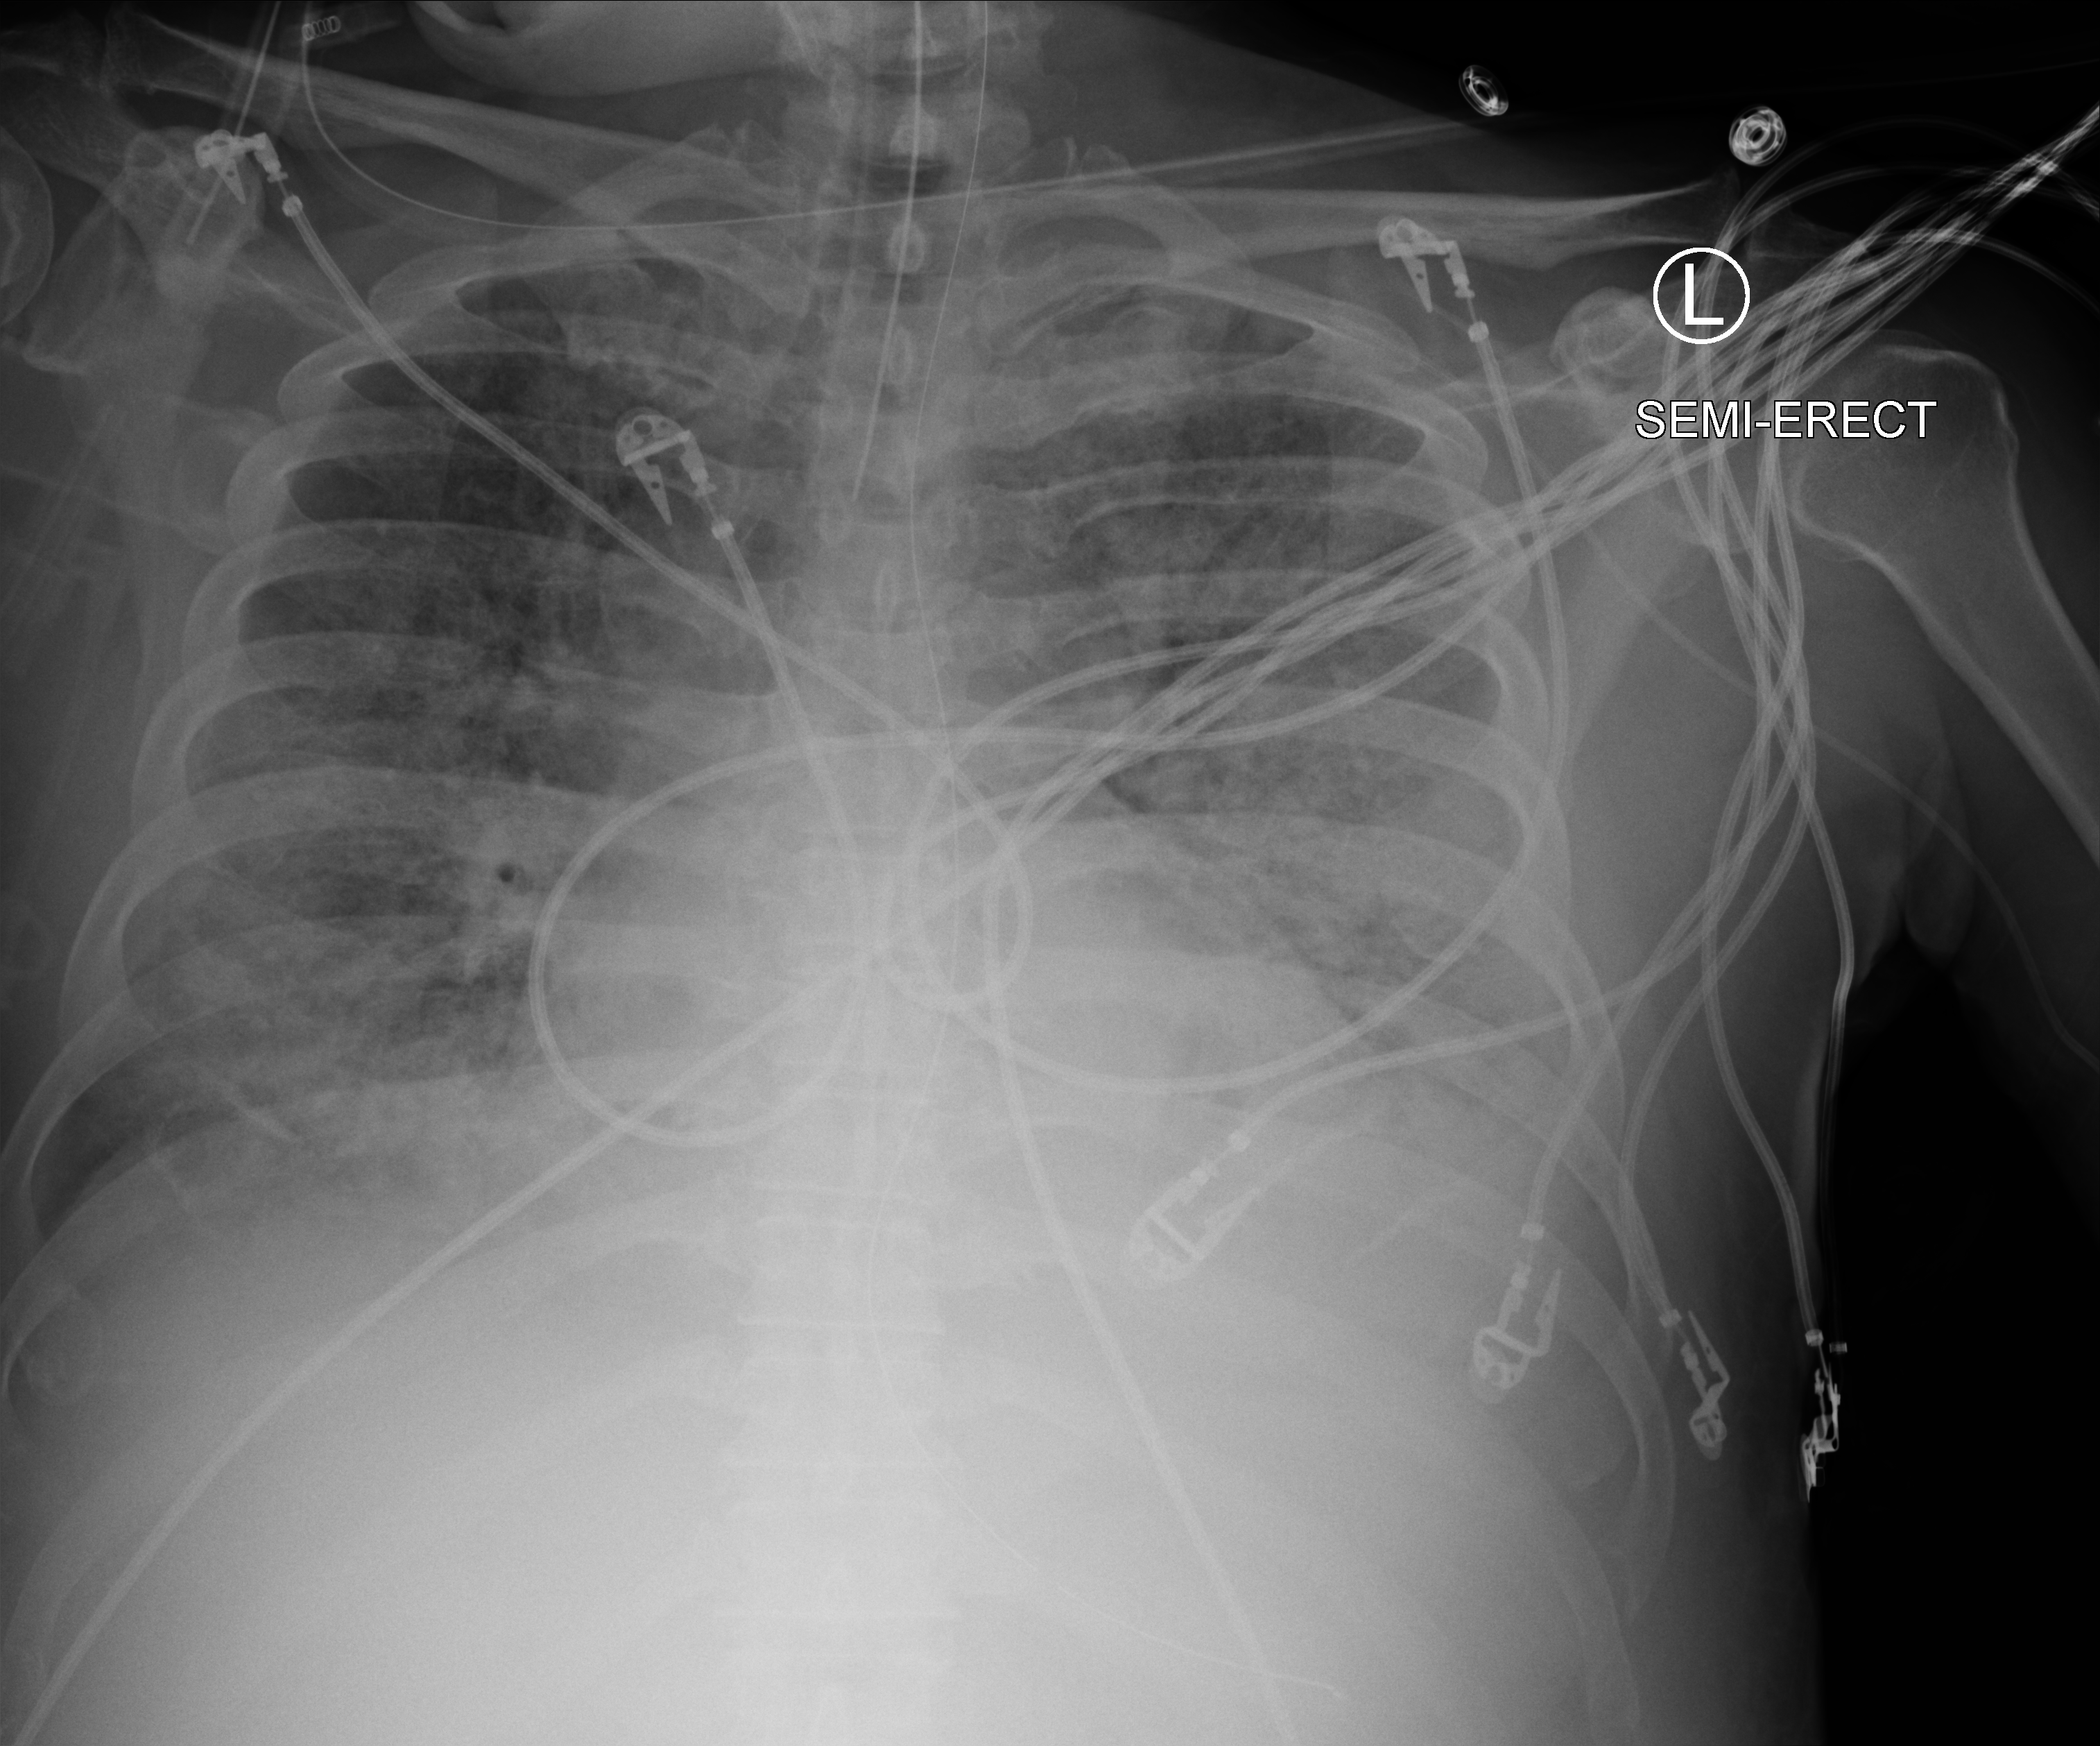
Portable chest radiograph. Patient hospitalised with COVID-19; male, aged 60–74 years.
Admission-level facts for this patient (not findings on this image; timing relative to this image not recorded): mechanically ventilated during this hospital stay: yes.